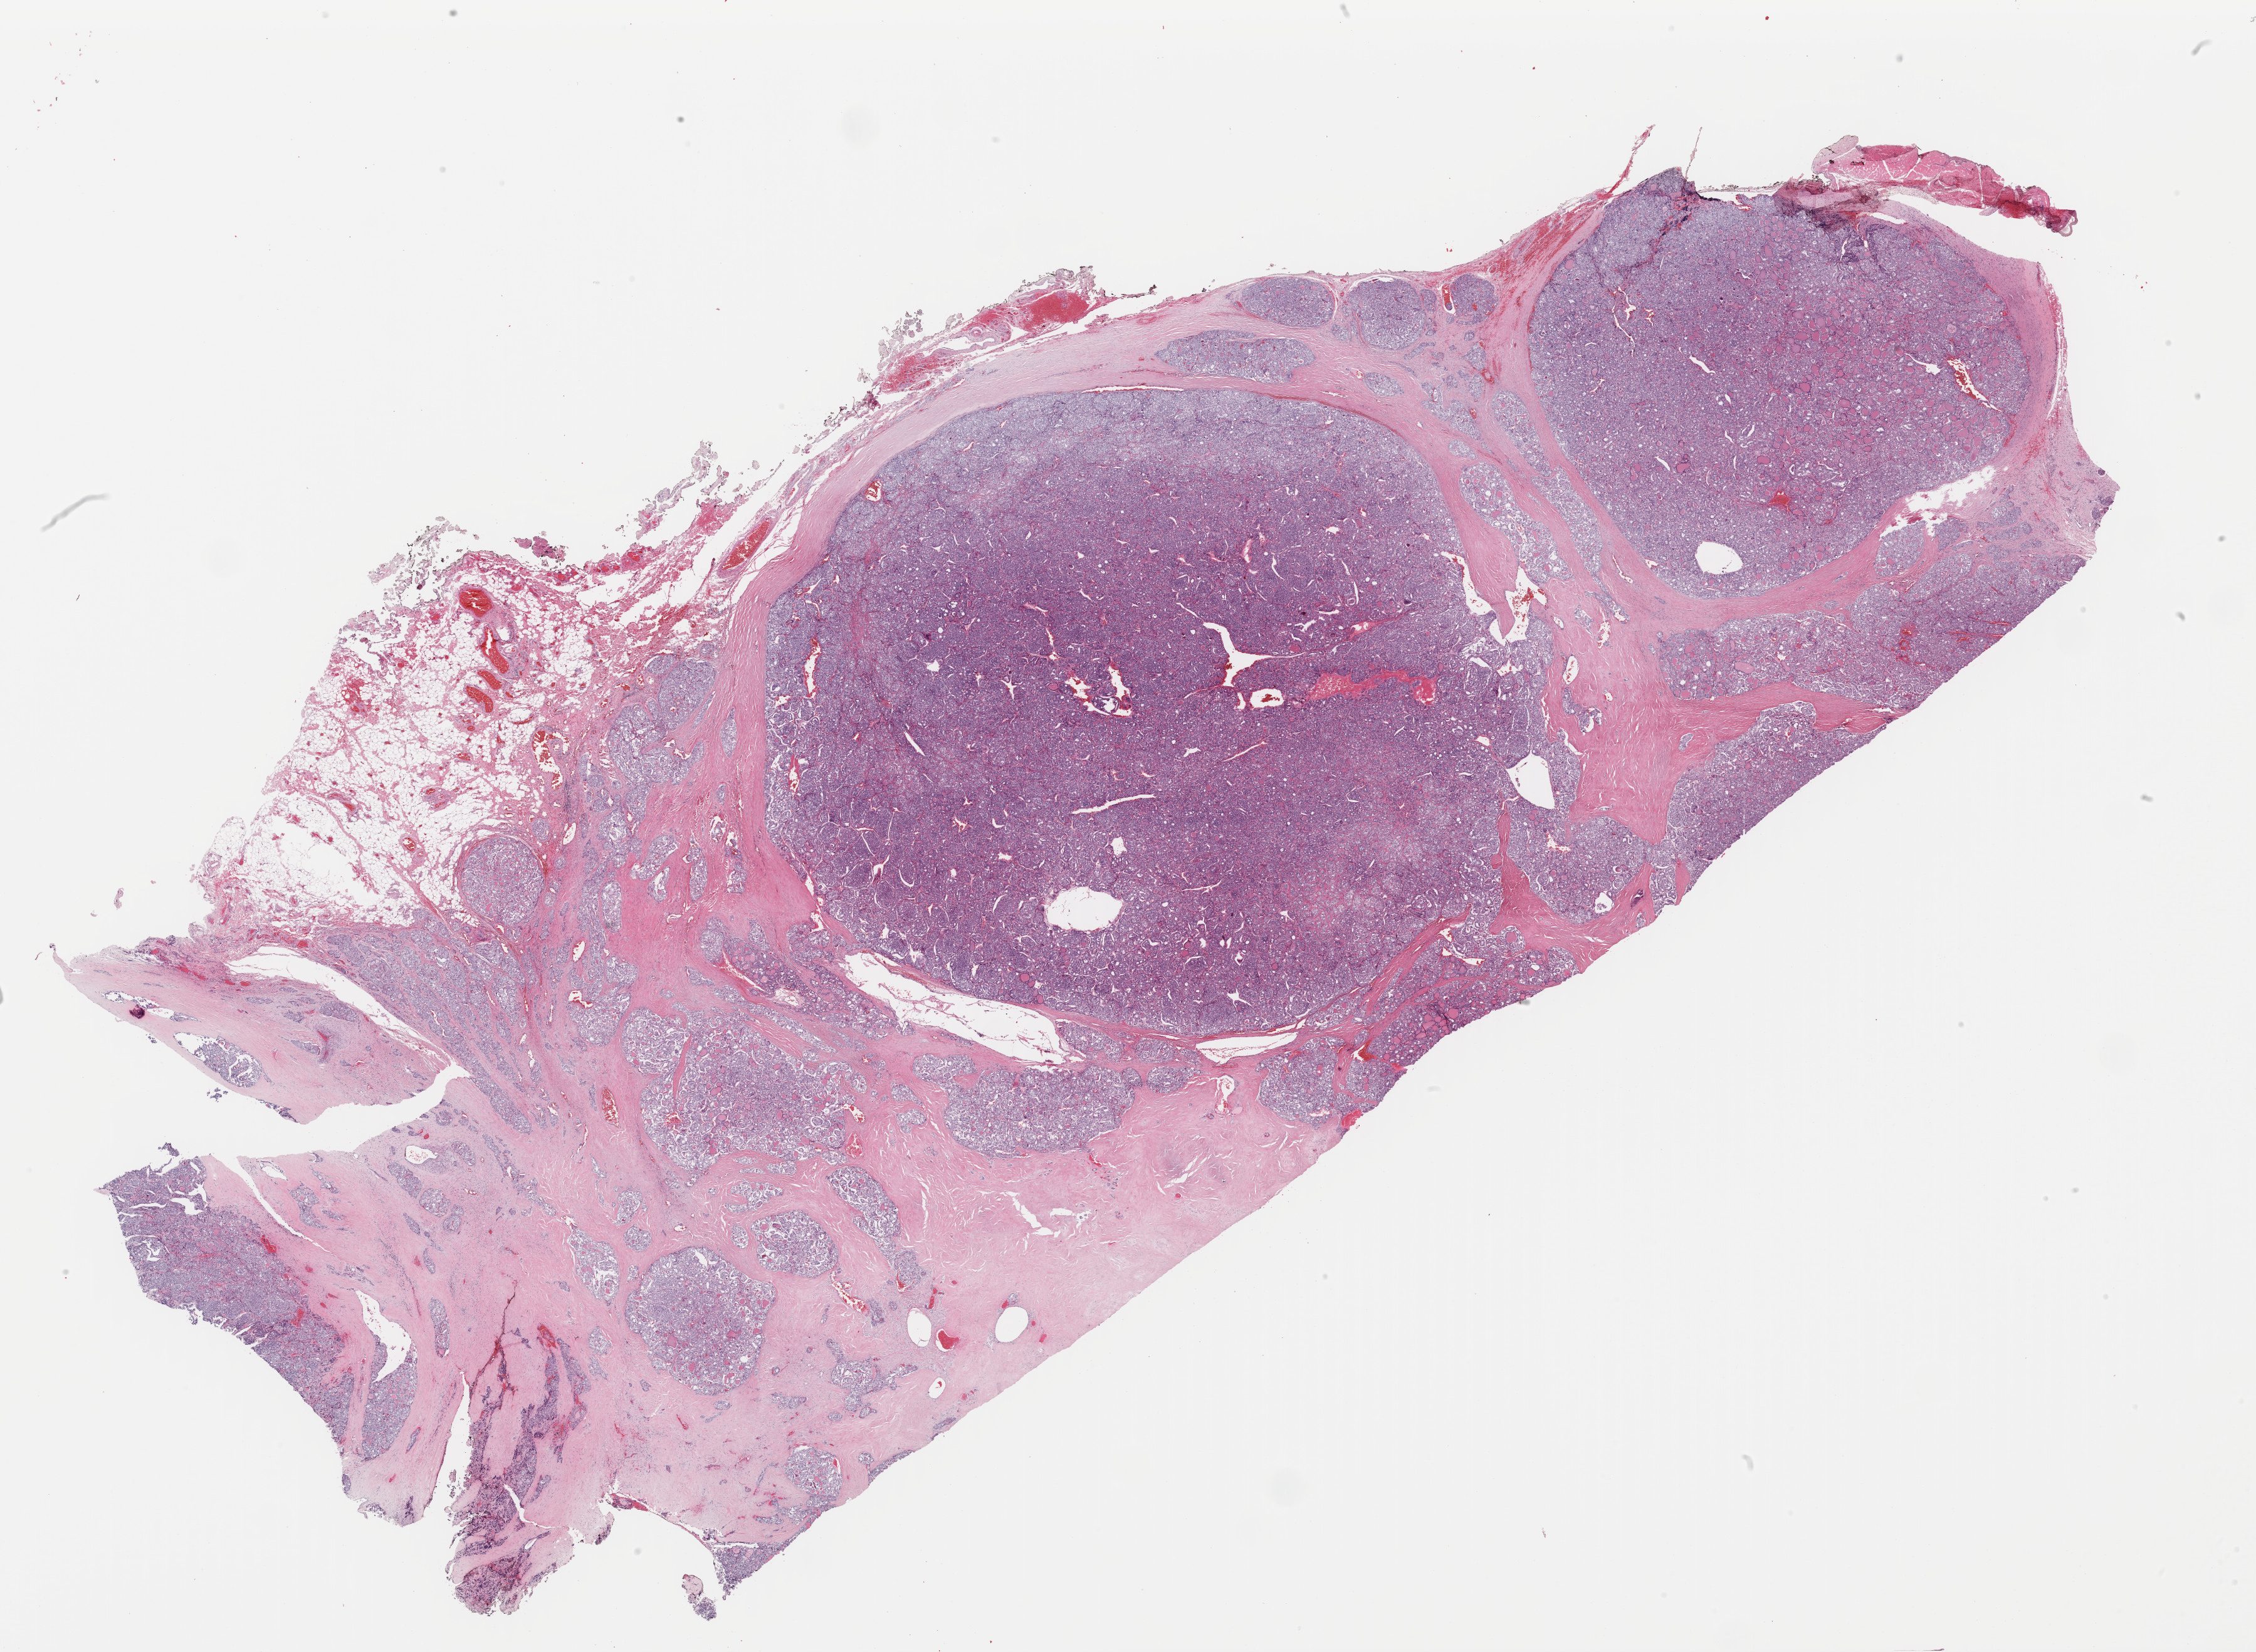
Whole-slide histology image, H&E-stained, whole scanned area (about 28.4 x 20.8 mm, acquisition: 40x scan) shown as a low-resolution overview; formalin-fixed paraffin-embedded (FFPE) diagnostic section; thyroid, primary tumour sample. Male patient; age at initial diagnosis 16 years.
- AJCC pathologic stage: II
- pathologic diagnosis: Papillary carcinoma, follicular variant (thyroid gland)
- laterality: left
- TNM: T4 N0 M1